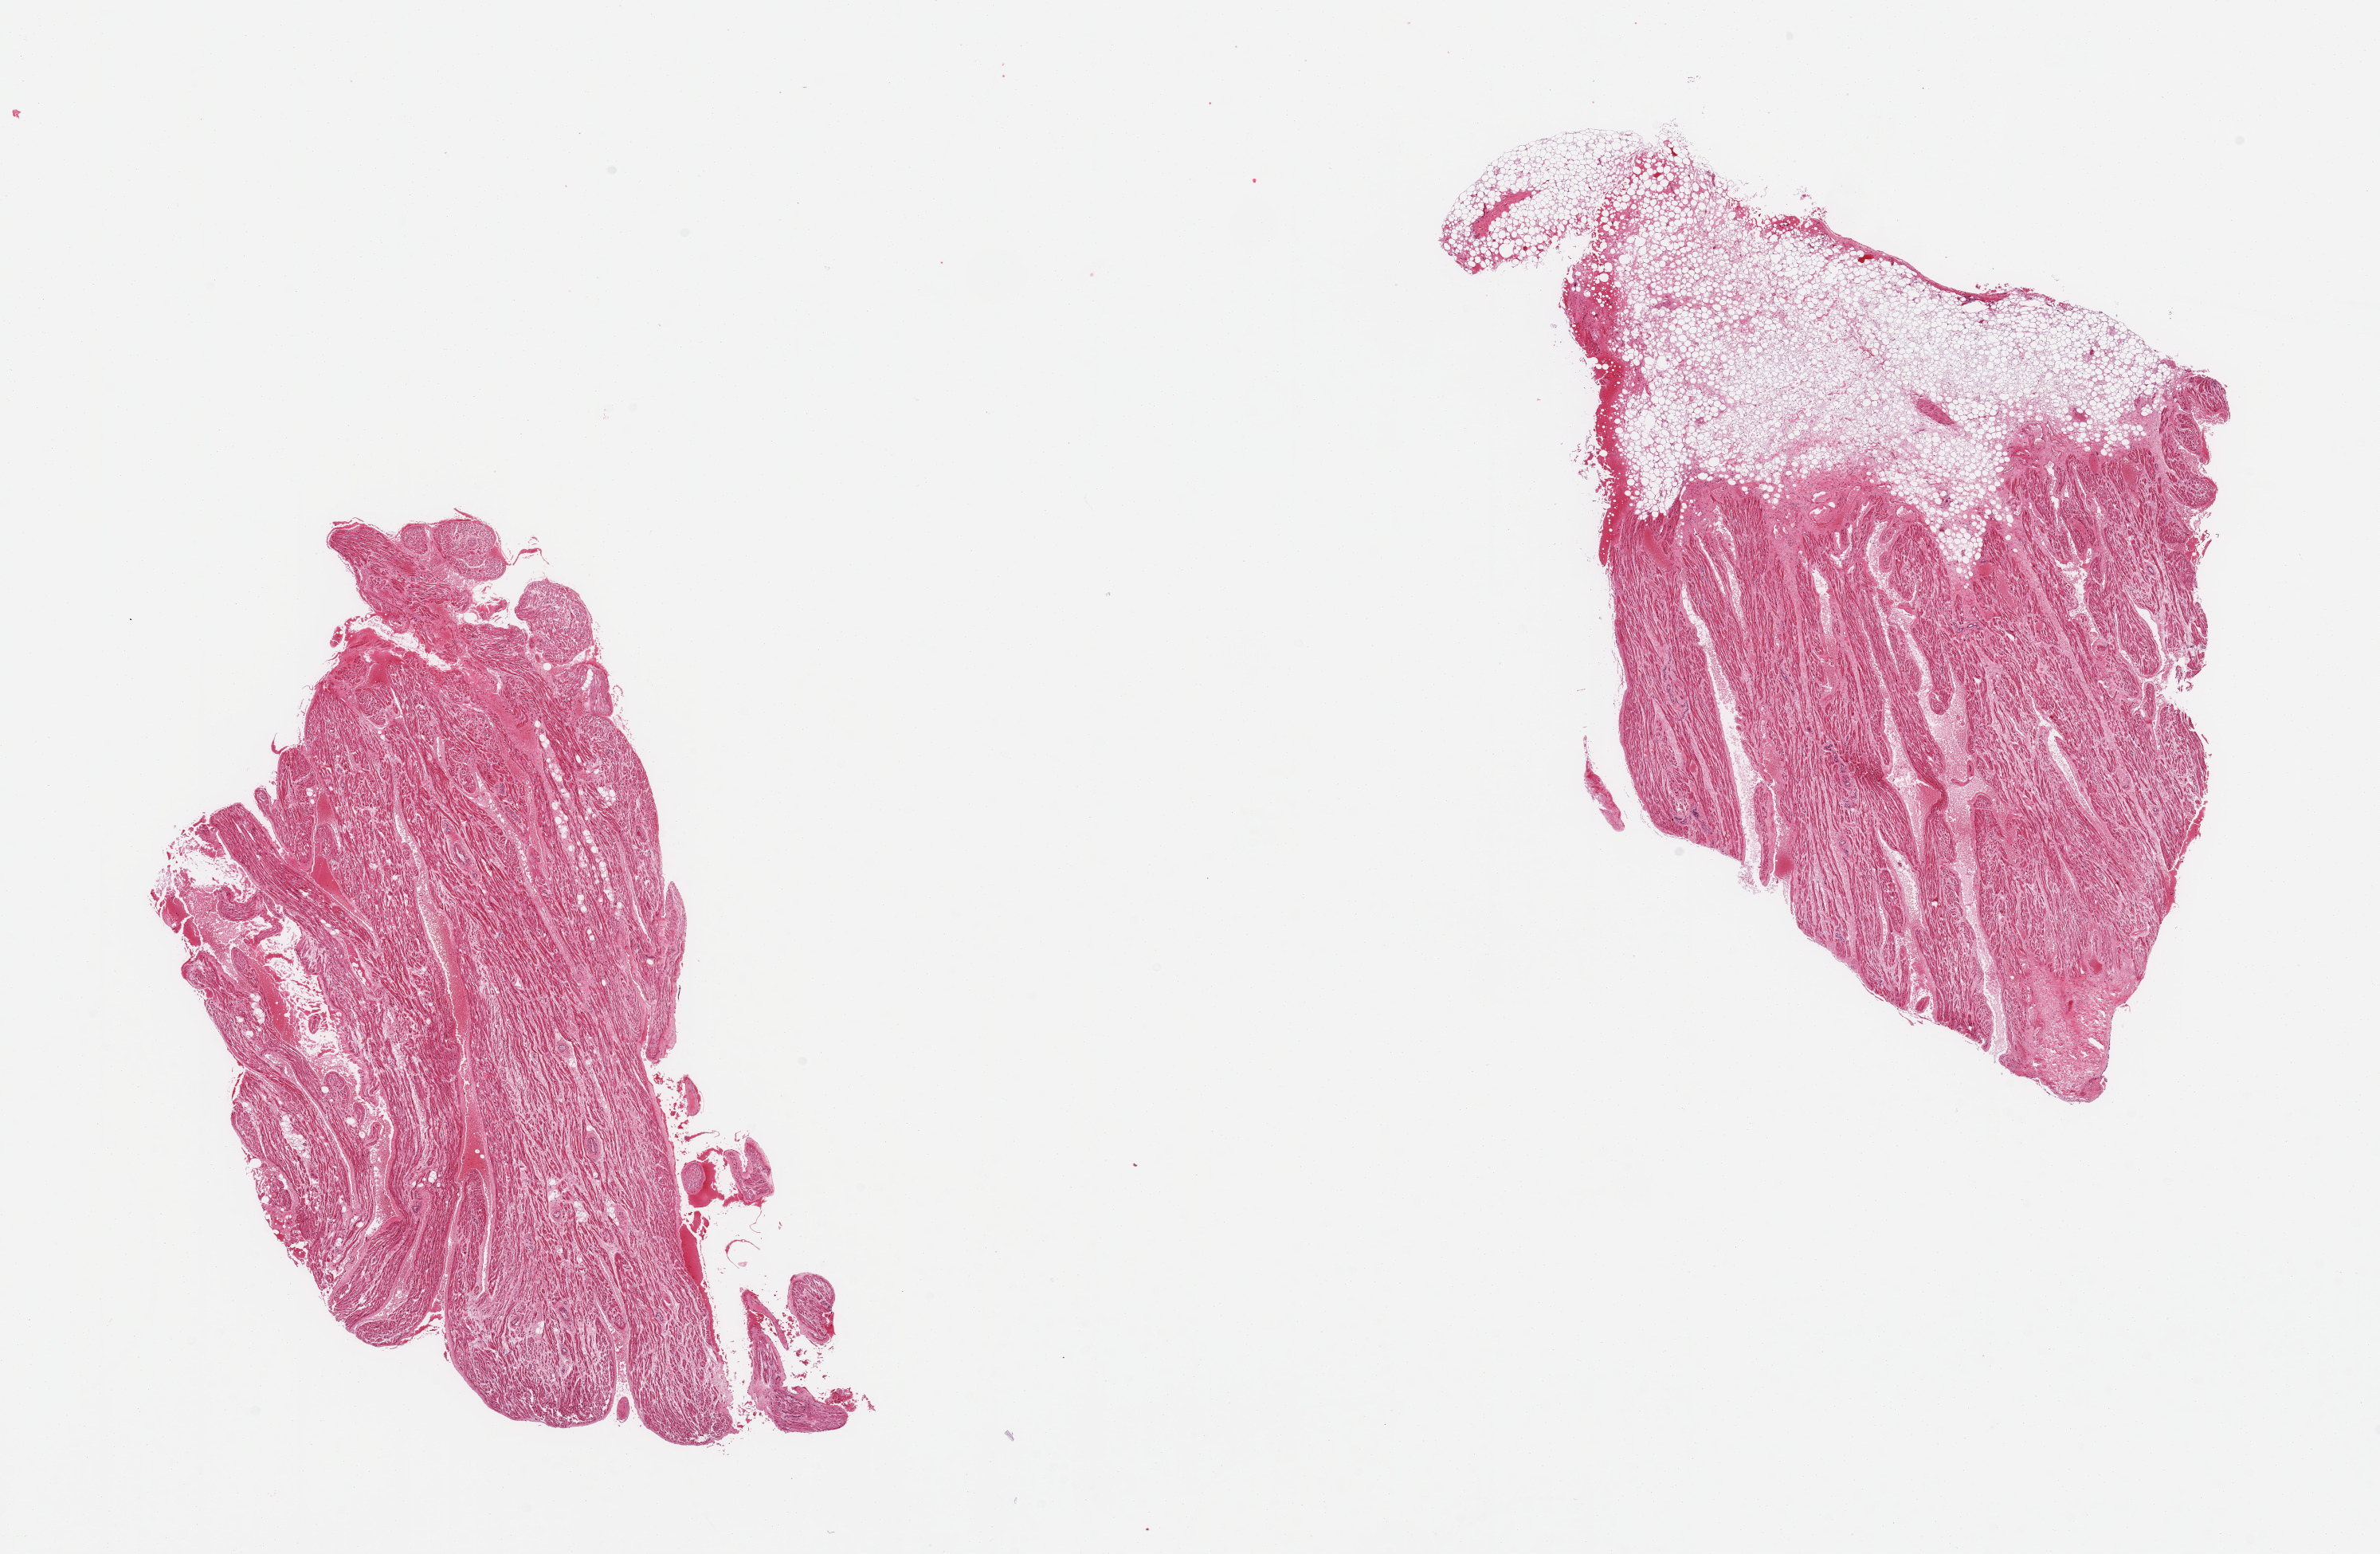
Whole-slide image, H&E stain, brightfield, low-resolution overview of the scanned area, about 23.6 x 15.4 mm (slide scanned at 20x); PAXgene-fixed, paraffin-embedded tissue; target tissue: auricular appendage; donor tissue sample.
Pathologist's review note for this sample: 2 pieces; 1 piece is ~40% fat, external.